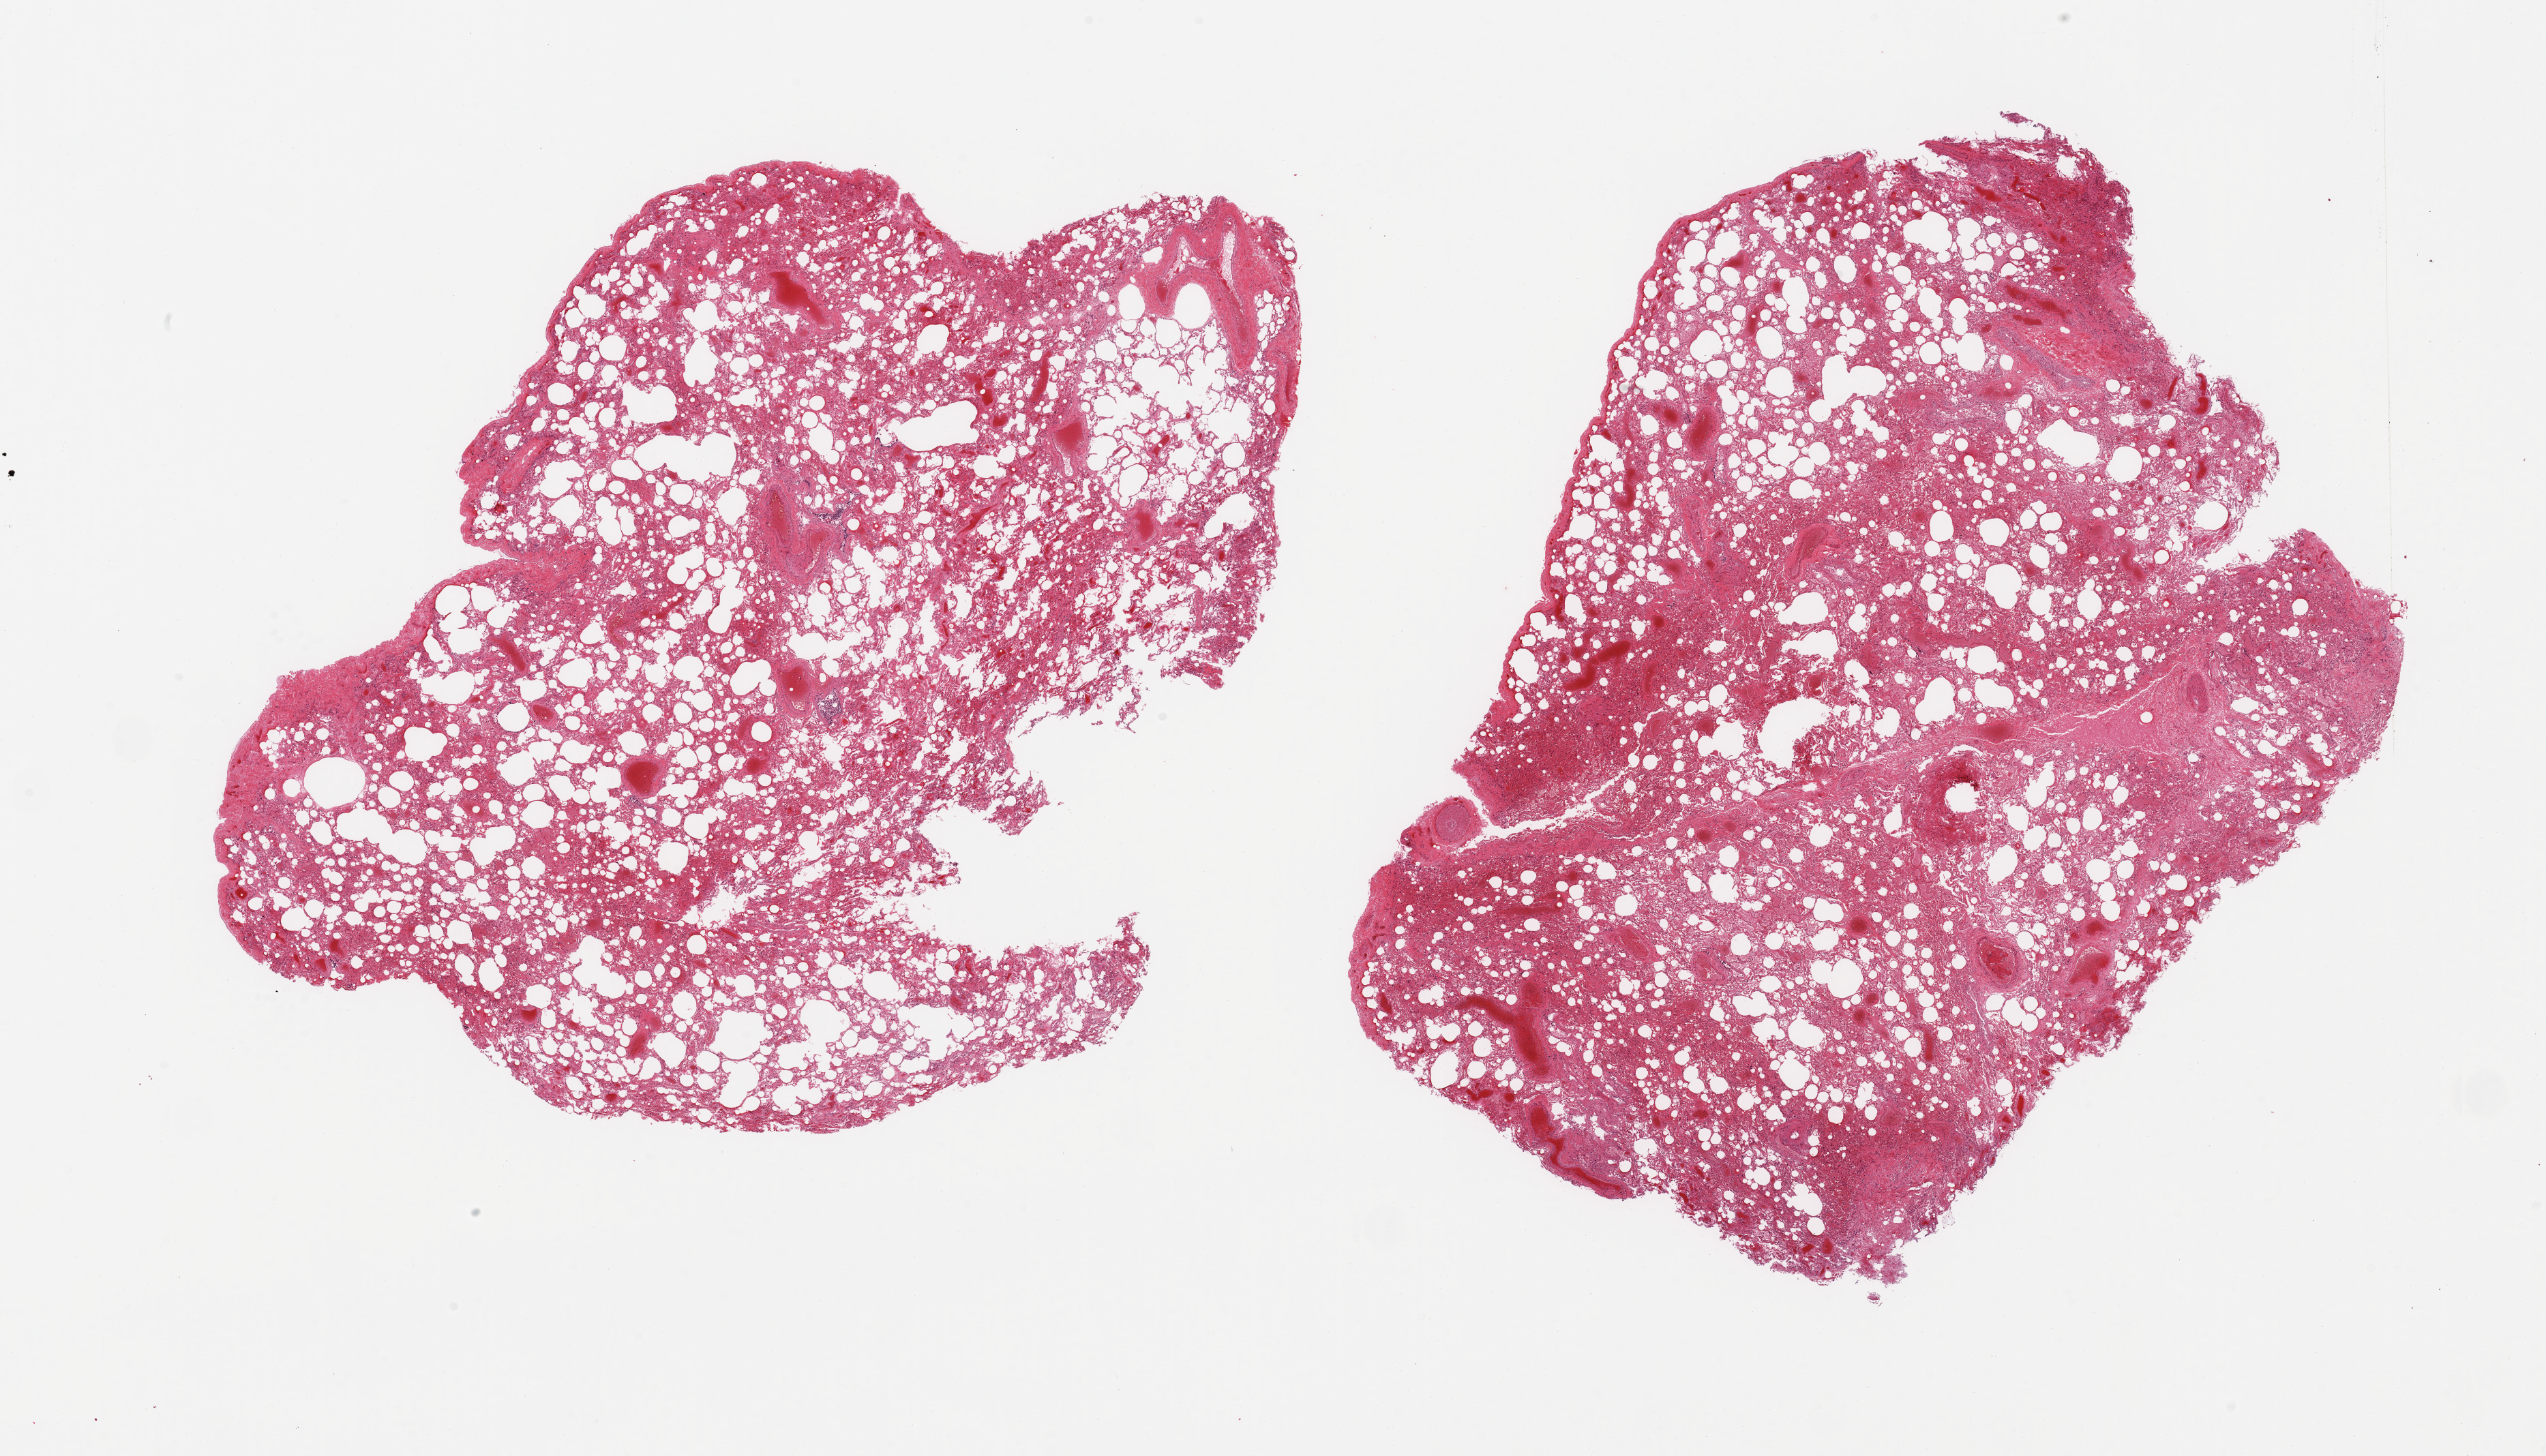
Digitized hematoxylin and eosin (H&E)-stained section — low-resolution overview of the scanned area, about 29.5 x 16.9 mm (slide scanned at 20x), PAXgene-fixed, paraffin-embedded tissue, target tissue: lung, tissue donor sample. Male donor.
Review note (as recorded): 2 pieces, moderate-marked congestion, focally organizing.